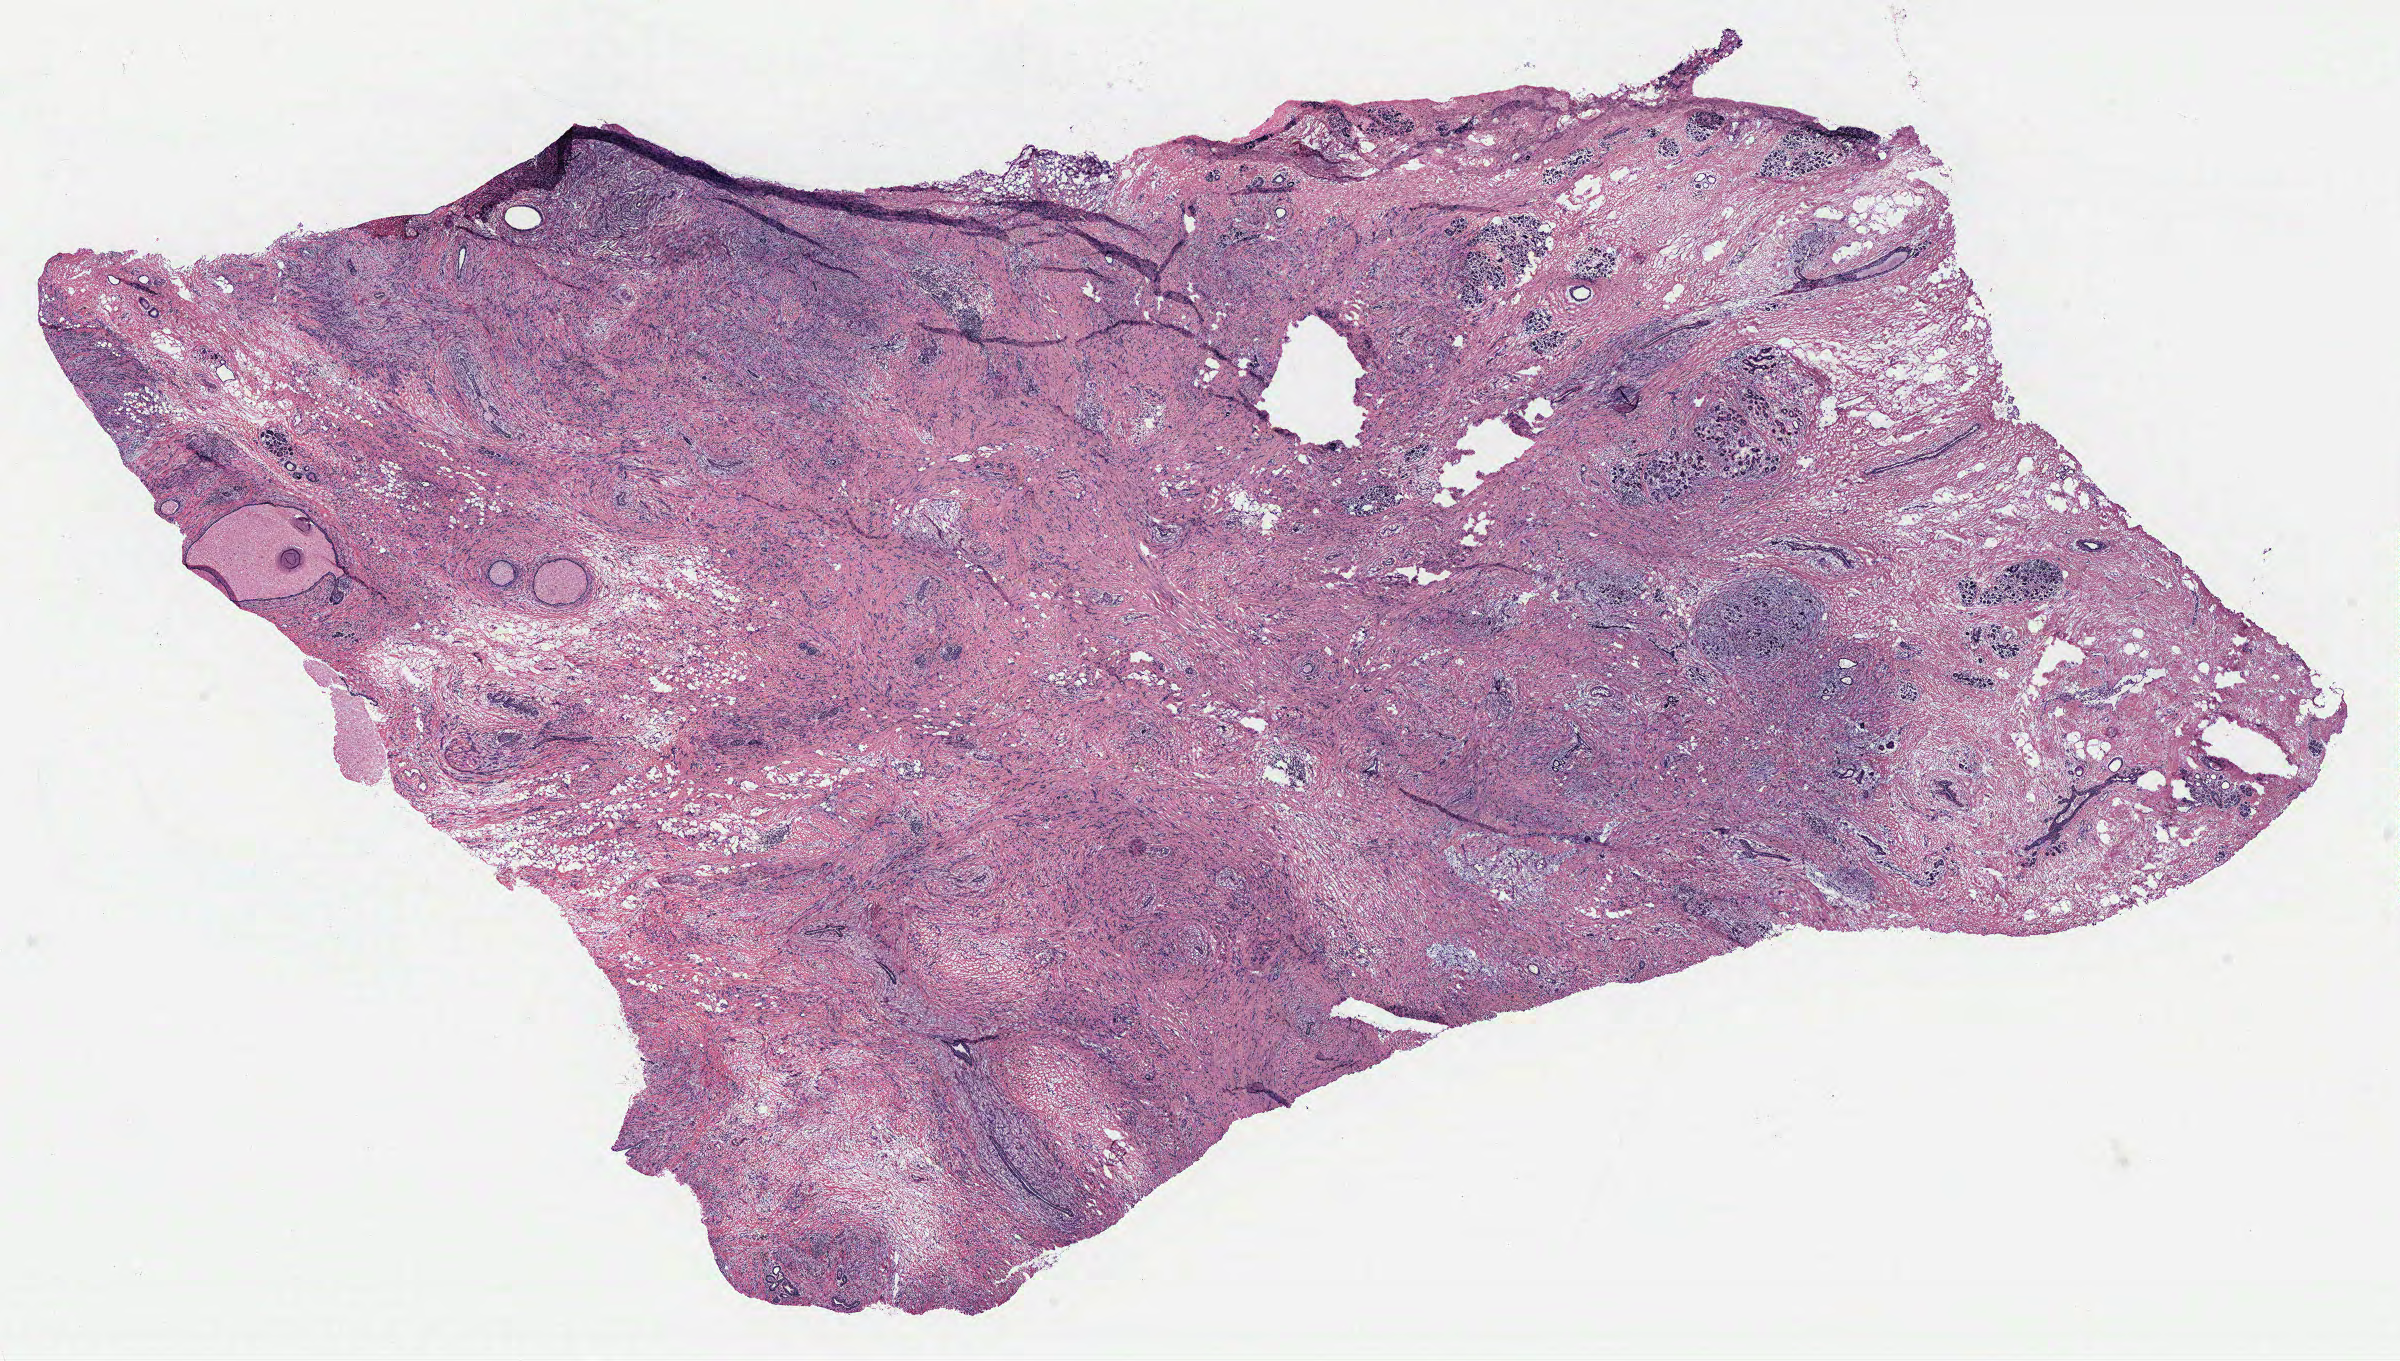
Whole-slide histology image, H&E-stained, shown as a low-resolution overview of the whole scanned area (about 19.2 x 10.9 mm, from a 40x scan), breast, tissue type not recorded. Patient: female, age 54 years.
Patient diagnosis: Infiltrating lobular carcinoma, NOS.